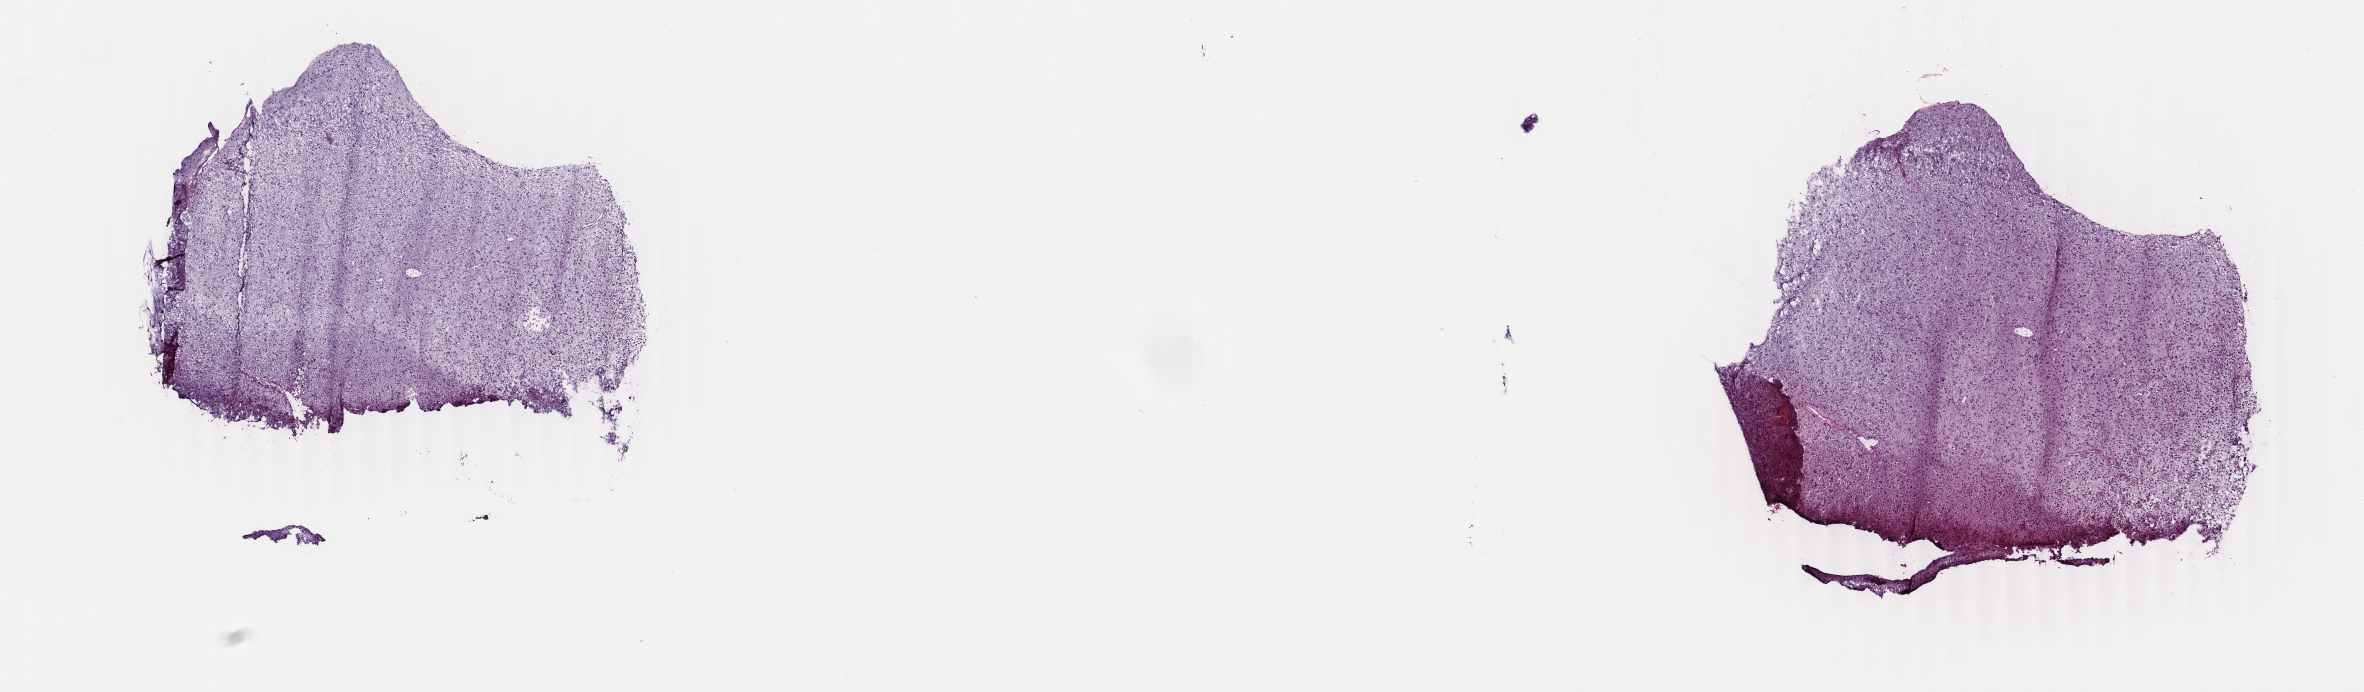
Whole-slide histology image, Hematoxylin and eosin (H&E) stained — a low-resolution overview of the entire scanned area, about 18.8 x 5.5 mm (acquisition: 40x scan); frozen section from the top of the tissue portion; primary tumour sample from the brain. Female, age 48 years at initial diagnosis. Histologic grade: G3 (poorly differentiated). Slide review estimates, as recorded: tumour cells 40%, tumour nuclei 75%, normal cells 10%, stromal cells 50%, necrosis 0%. Infiltration values recorded for this section: lymphocyte infiltration 0%, monocyte infiltration 0%, neutrophil infiltration 0%.
• histologic diagnosis: Astrocytoma, anaplastic
• laterality: right